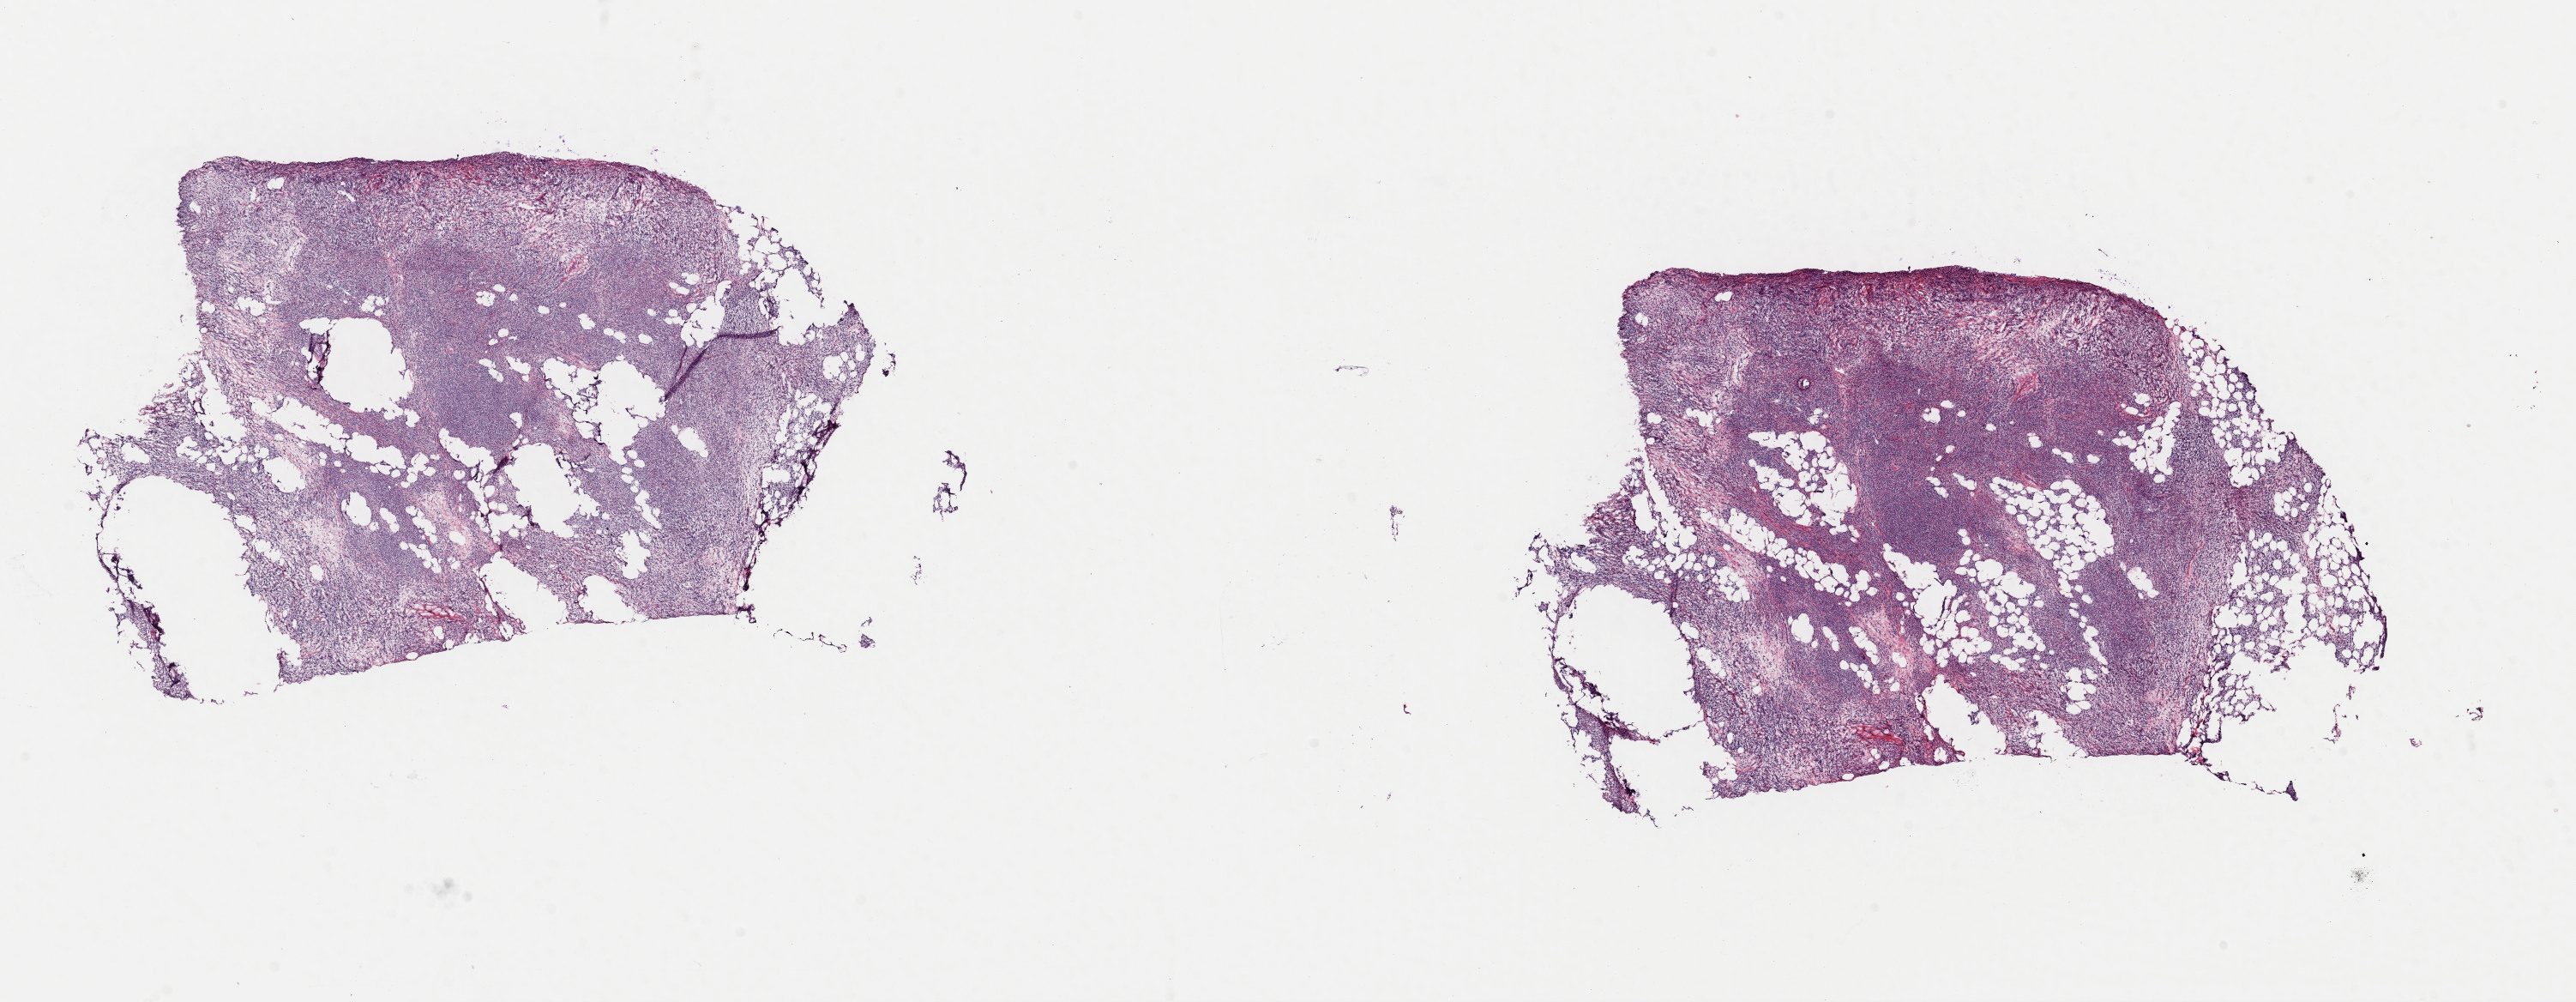
Whole-slide histology image, H&E-stained, shown as a low-resolution overview of the whole scanned area (about 23.7 x 9.2 mm, from a 40x scan). Frozen section. Breast, primary tumour sample. Female patient; age at initial diagnosis 63 years. Composition of this section per pathologist review: tumour cells 80%, tumour nuclei 90%, normal cells 0%, stromal cells 20%, necrosis 0%. Inflammatory infiltration, as recorded: lymphocyte infiltration 0%, monocyte infiltration 0%, neutrophil infiltration 0%.
• laterality: right
• AJCC pathologic stage: IIB (7th edition)
• diagnosis: Lobular carcinoma, NOS